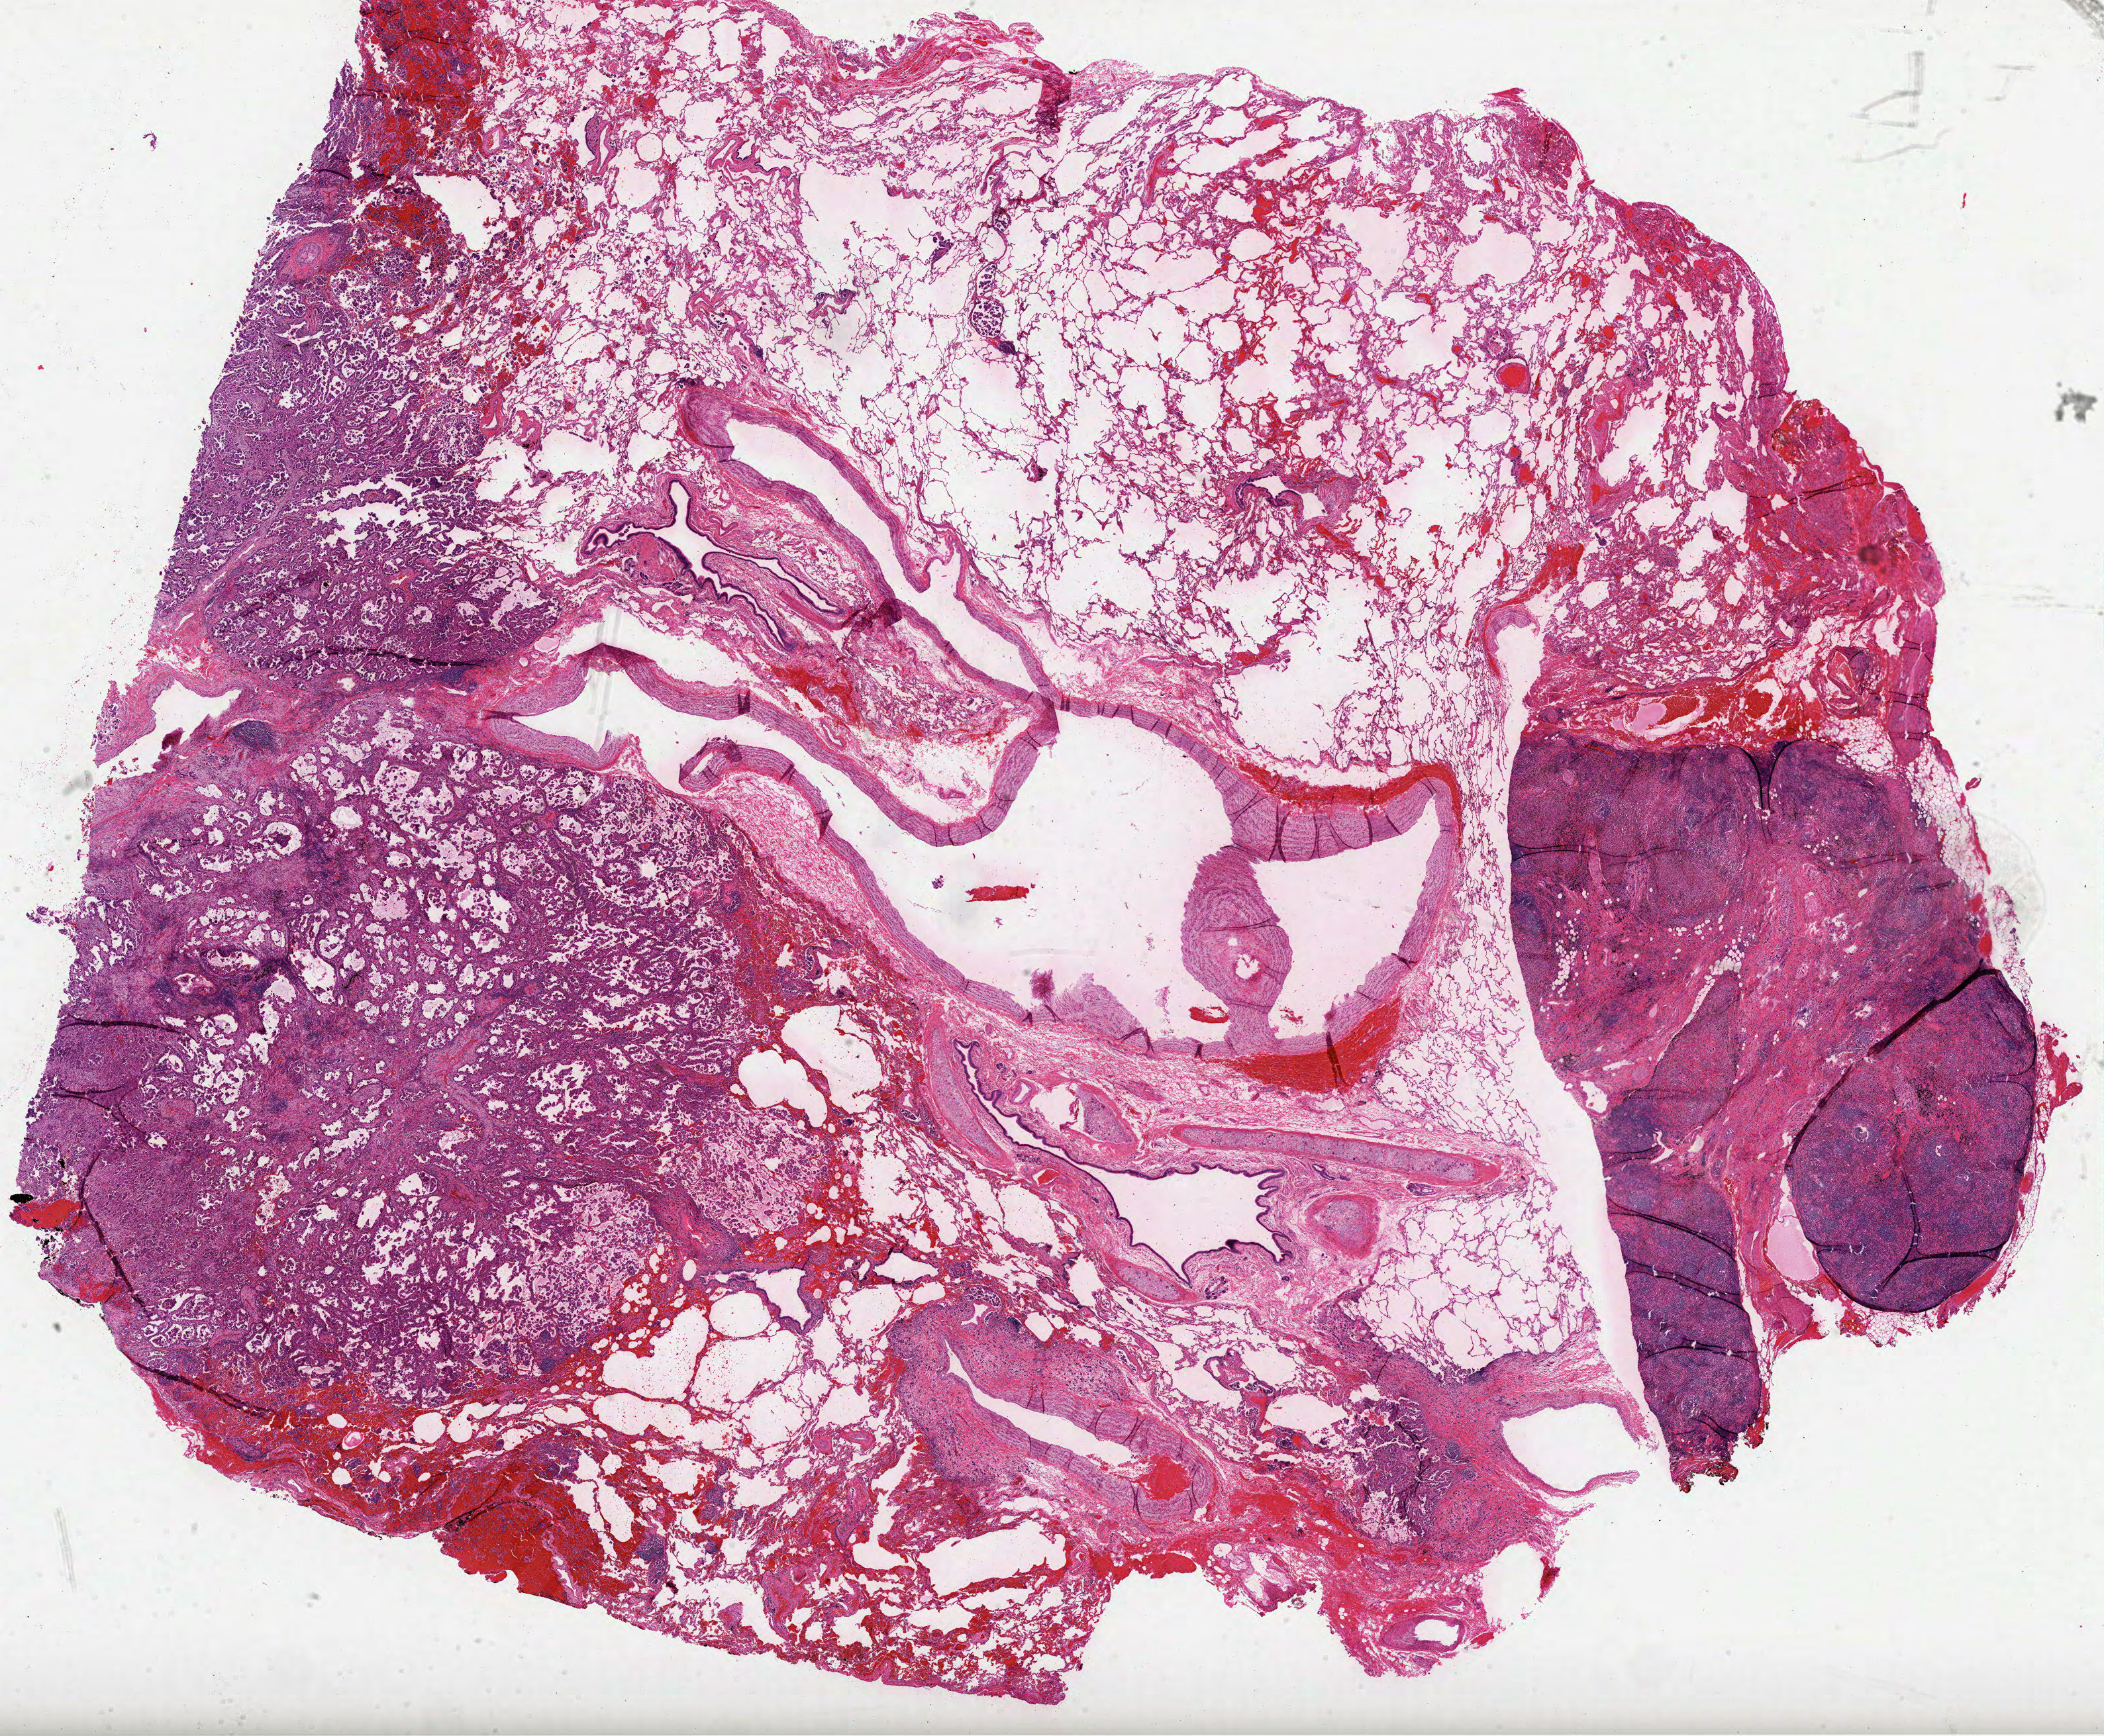
Digitized H&E-stained tissue section (whole slide), a low-resolution overview of the entire scanned area, about 25.6 x 21.1 mm (acquisition: 40x scan). Formalin-fixed paraffin-embedded (FFPE) diagnostic section. Lung, primary tumour sample. Patient: female, age at initial diagnosis 69 years.
Histologic diagnosis: Adenocarcinoma, NOS (middle lobe, lung).